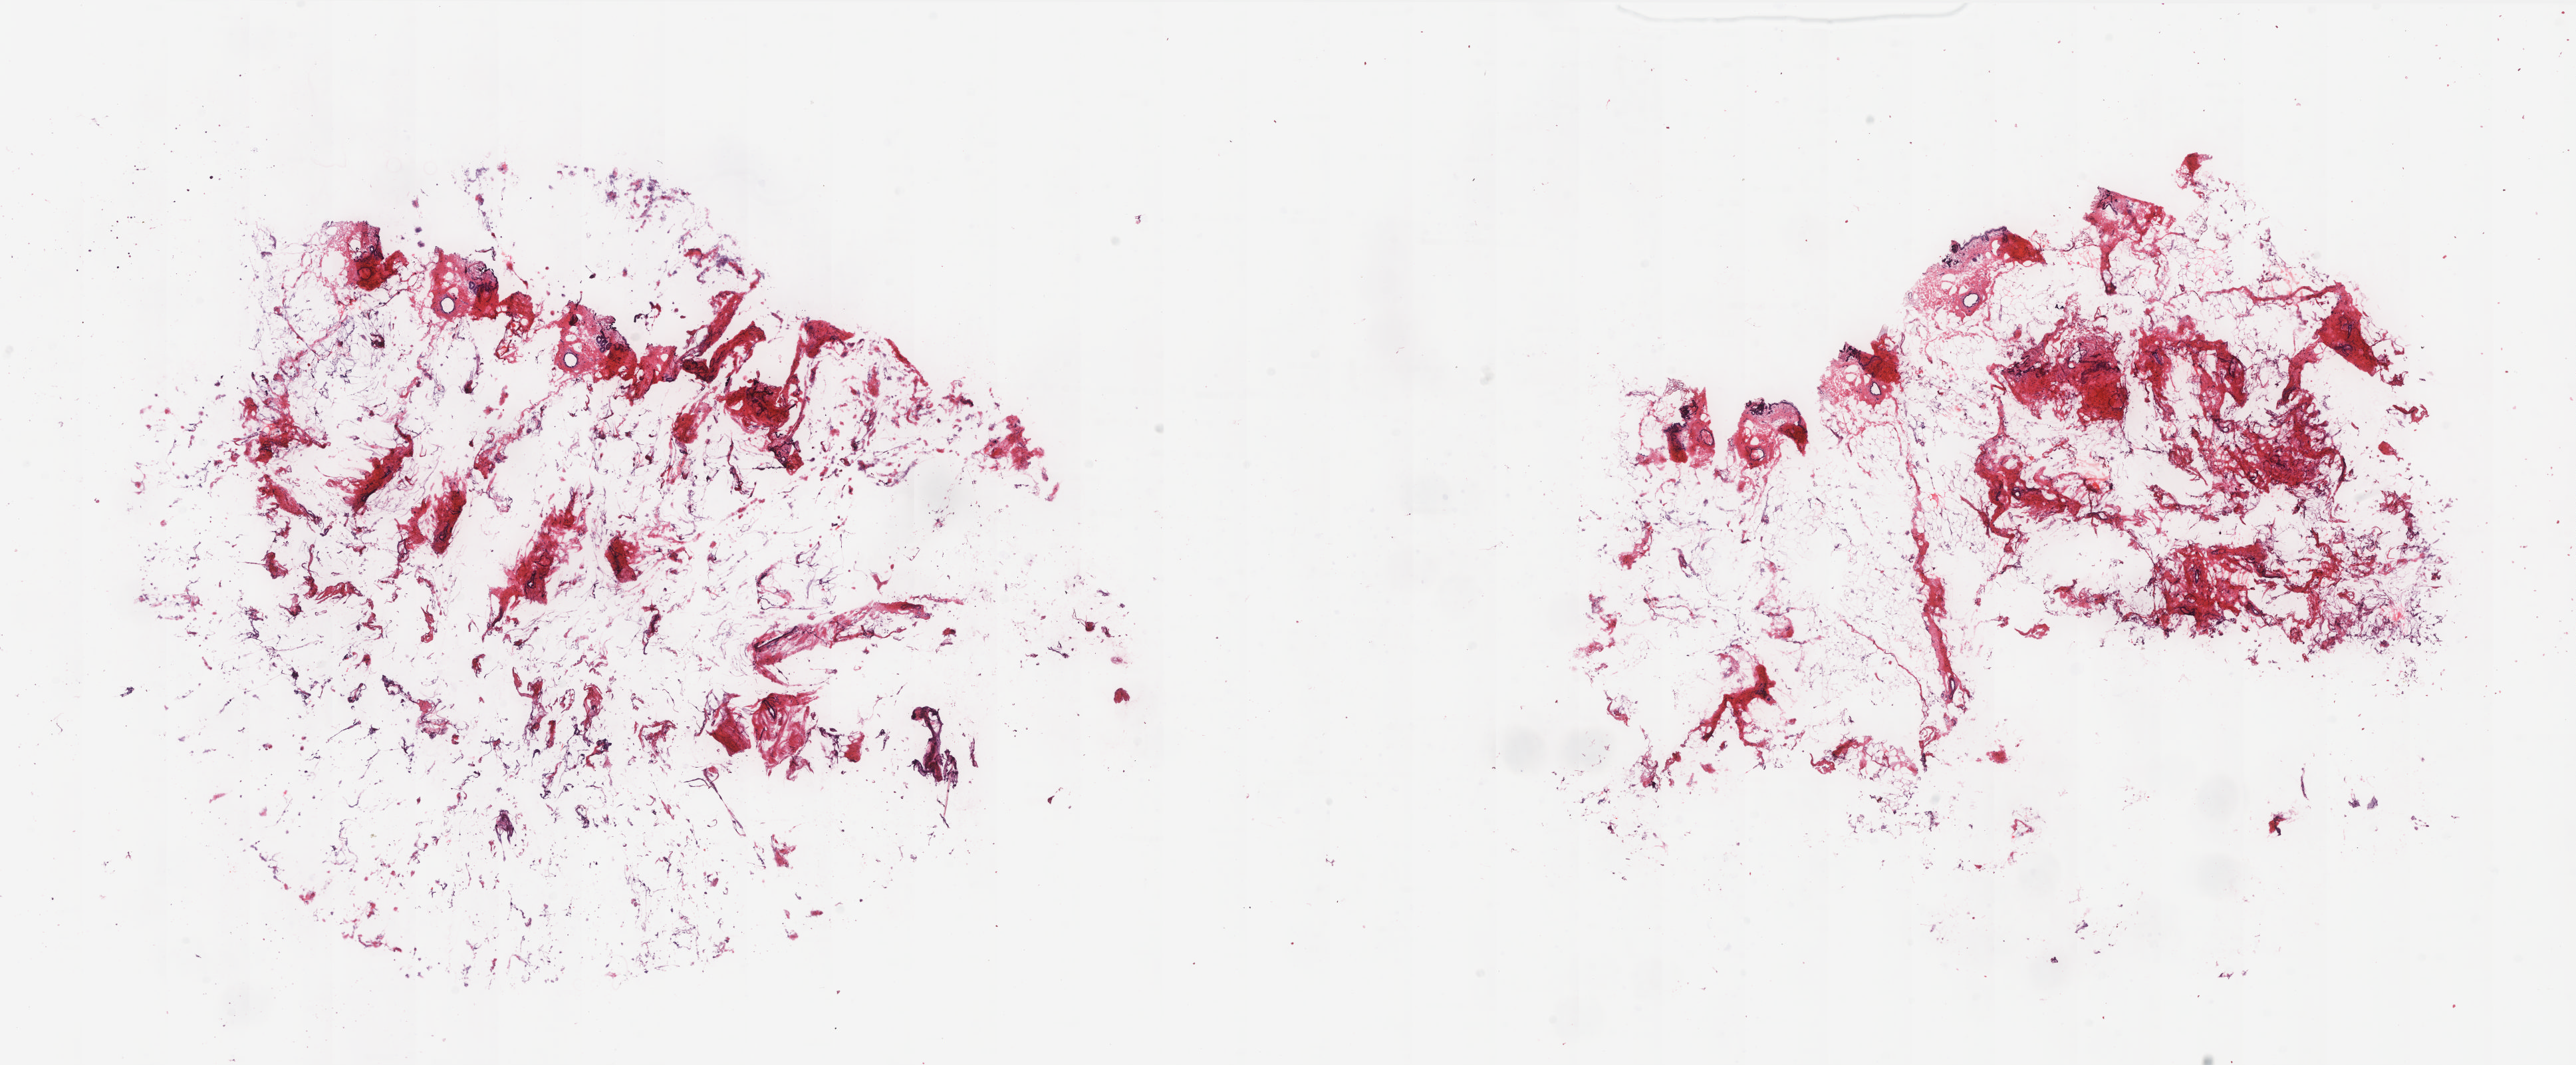
Whole-slide histology image, Hematoxylin and eosin (H&E) stained, a low-resolution overview of the entire scanned area, about 30.9 x 12.8 mm (acquisition: 20x scan); frozen section; solid tissue normal (non-tumour tissue) sample from the breast. Female, age 79 years at initial diagnosis. Pathologist review of this section (percent, as recorded): tumour cells 0%, tumour nuclei 0%.
This section: solid tissue normal (non-tumour) sample from the same patient. Patient diagnosis: Infiltrating duct carcinoma, NOS.